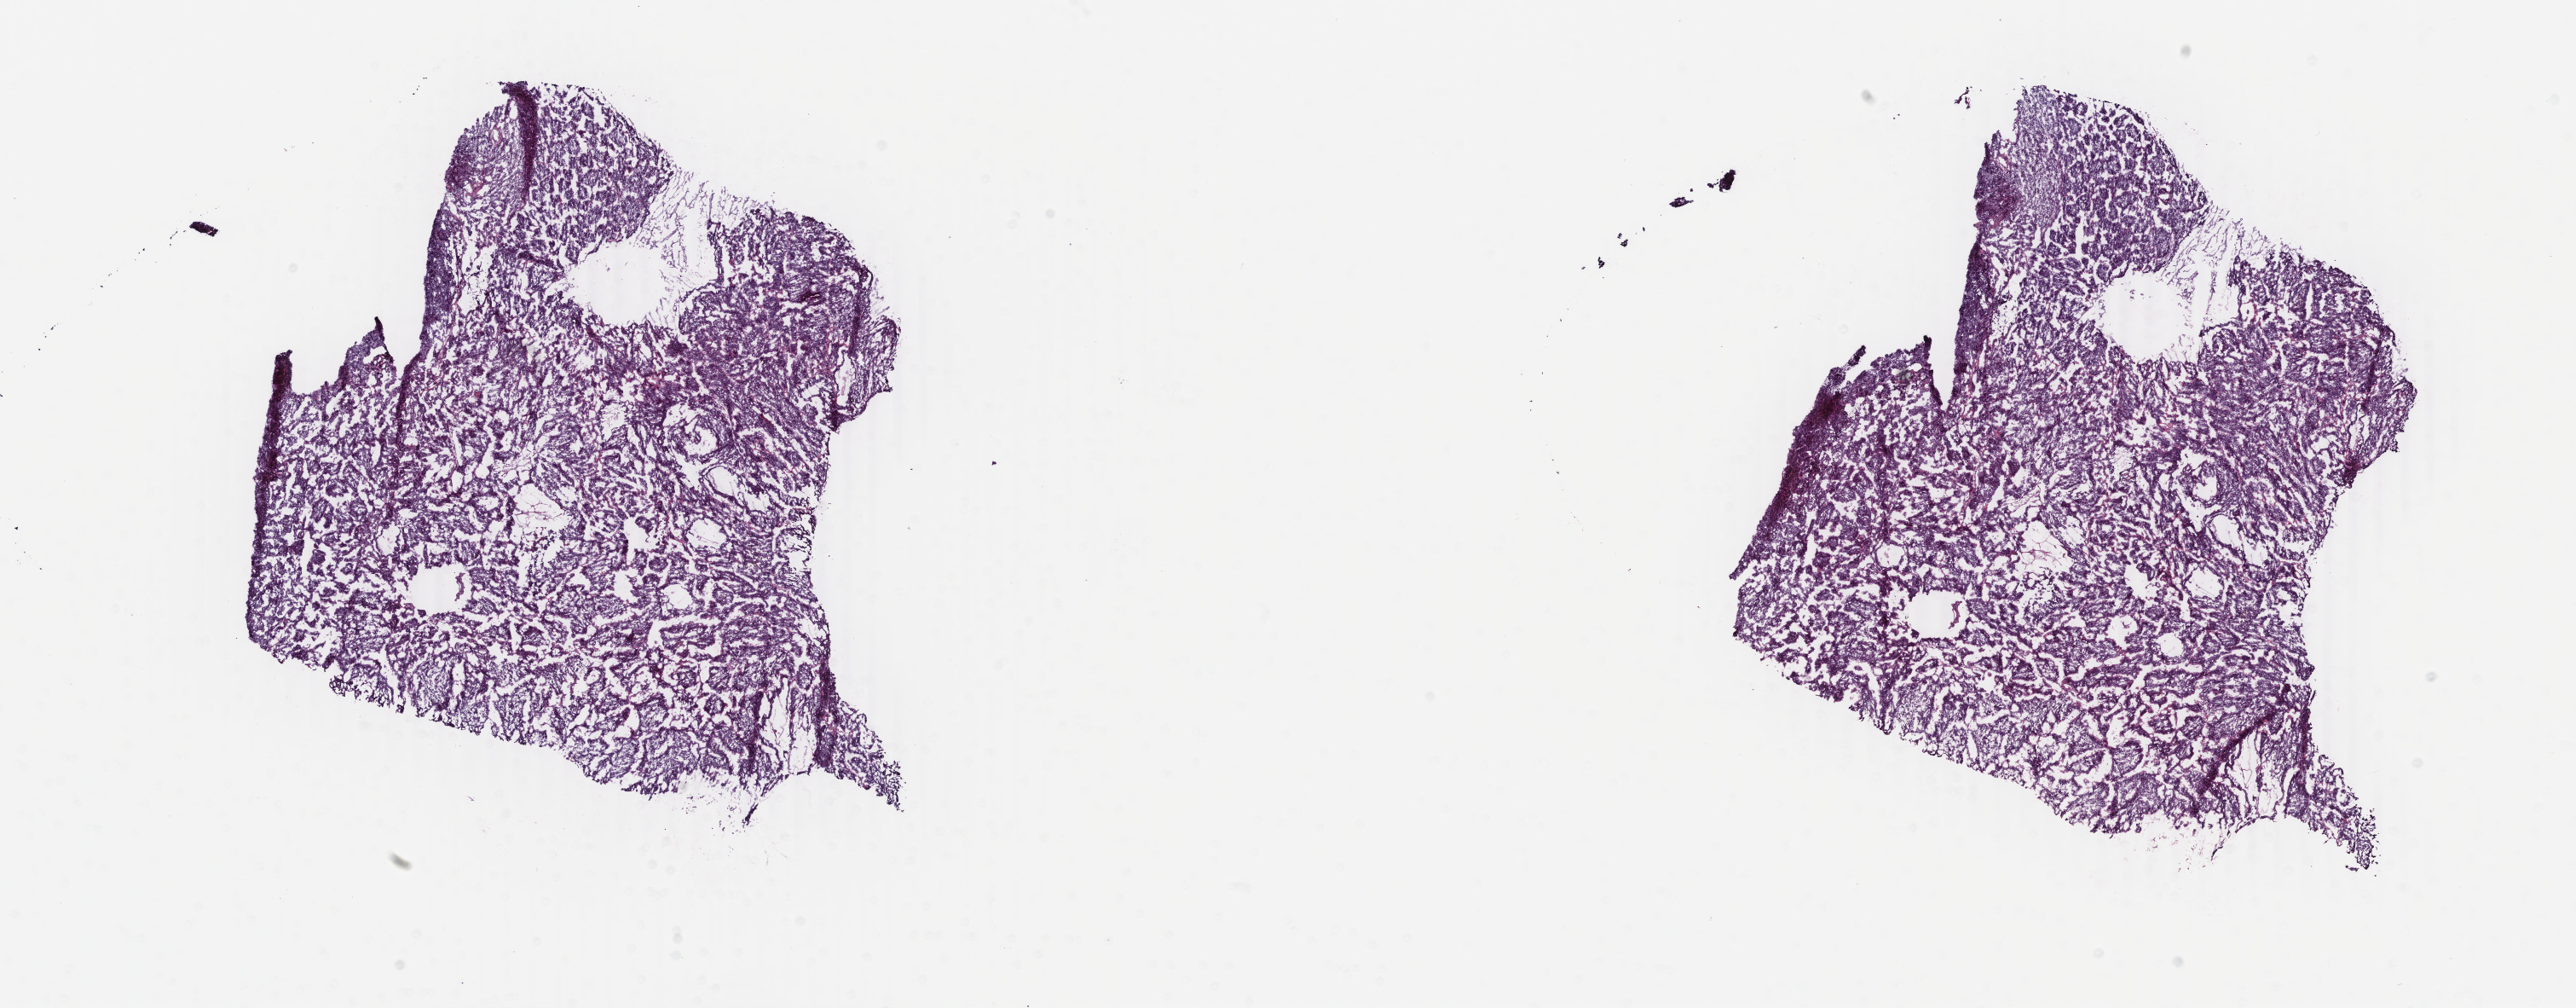
Digitized Hematoxylin and eosin (H&E) stained tissue section (whole slide) — whole scanned area (about 24.0 x 9.4 mm) shown as a low-resolution overview, frozen section from the bottom of the tissue portion, liver, primary tumour sample. Patient: female, age at initial diagnosis 24 years. Histologic grade: G1 (well differentiated). Pathologist review of this section (percent, as recorded): tumour cells 100%, tumour nuclei 95%, normal cells 0%, stromal cells 0%, necrosis 0%. Inflammatory infiltration, as recorded: lymphocyte infiltration 0%, monocyte infiltration 0%, neutrophil infiltration 0%.
Histologic diagnosis: Hepatocellular carcinoma, NOS. AJCC pathologic stage: IIIA (6th edition).